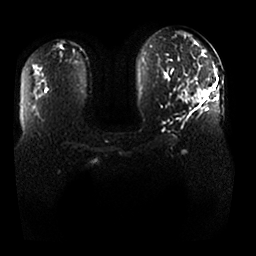
Breast MRI, one axial slice; position 16 of 25 along the scan axis; diffusion-weighted series; image 2 of 4 stored at this slice position (different b-values; order by instance number); 1.5 T; 4 mm slice thickness; 256 × 256 image matrix. Female patient.
Structures marked on this image (expert manual segmentation):
- tumour on diffusion-weighted imaging: box from (x=195, y=89) to (x=212, y=100) px